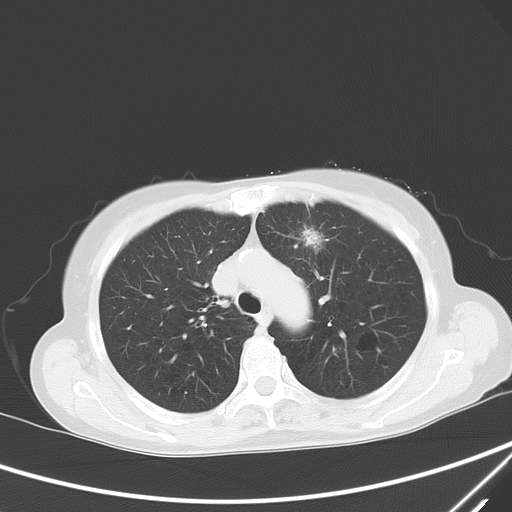
Chest CT, one axial slice; slice 45 of 60 in the series (ordered by position); 120 kVp; lung window (W 1500 / L -600 HU); 512 × 512 image matrix, field of view 350 × 350 mm. Female patient, age 71 years. Case-level facts recorded for this patient, not image findings: clinical TNM (as recorded): T1c N0 M0; histopathological grade: G2-3.
Outlined on this slice (bounding box drawn by a radiologist):
- lung tumour (recorded histology: adenocarcinoma): bounding box <296,221,332,256> (left, top, right, bottom; pixels)